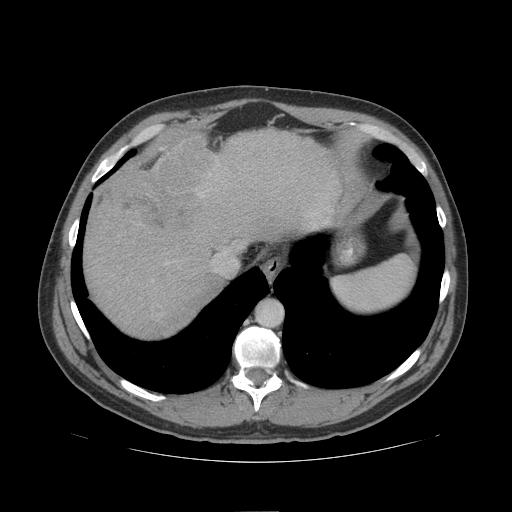
Contrast-enhanced abdominal CT (liver protocol), one axial slice; position 85 of 109 along the scan axis; reconstruction kernel STANDARD; soft-tissue window (W 400 / L 40 HU); 512 × 512 image matrix, field of view 420 × 420 mm. From the clinical record (not read from this slice): diagnosis: hepatocellular carcinoma (patient treated with transarterial chemoembolisation; whether this scan precedes or follows treatment is not stated here); TNM stage (as recorded): Stage-IIIB; Child-Pugh class: A; tumour nodularity: multinodular.
Structures marked on this image (semi-automatically segmented with operator editing):
- abdominal aorta: bounding box <258,302,282,327> (left, top, right, bottom; pixels)
- liver parenchyma outside the tumour (the mass and vessels are separate outlines, so this box may not span the whole liver): <84,128,350,336>
- mass: <105,133,217,236>